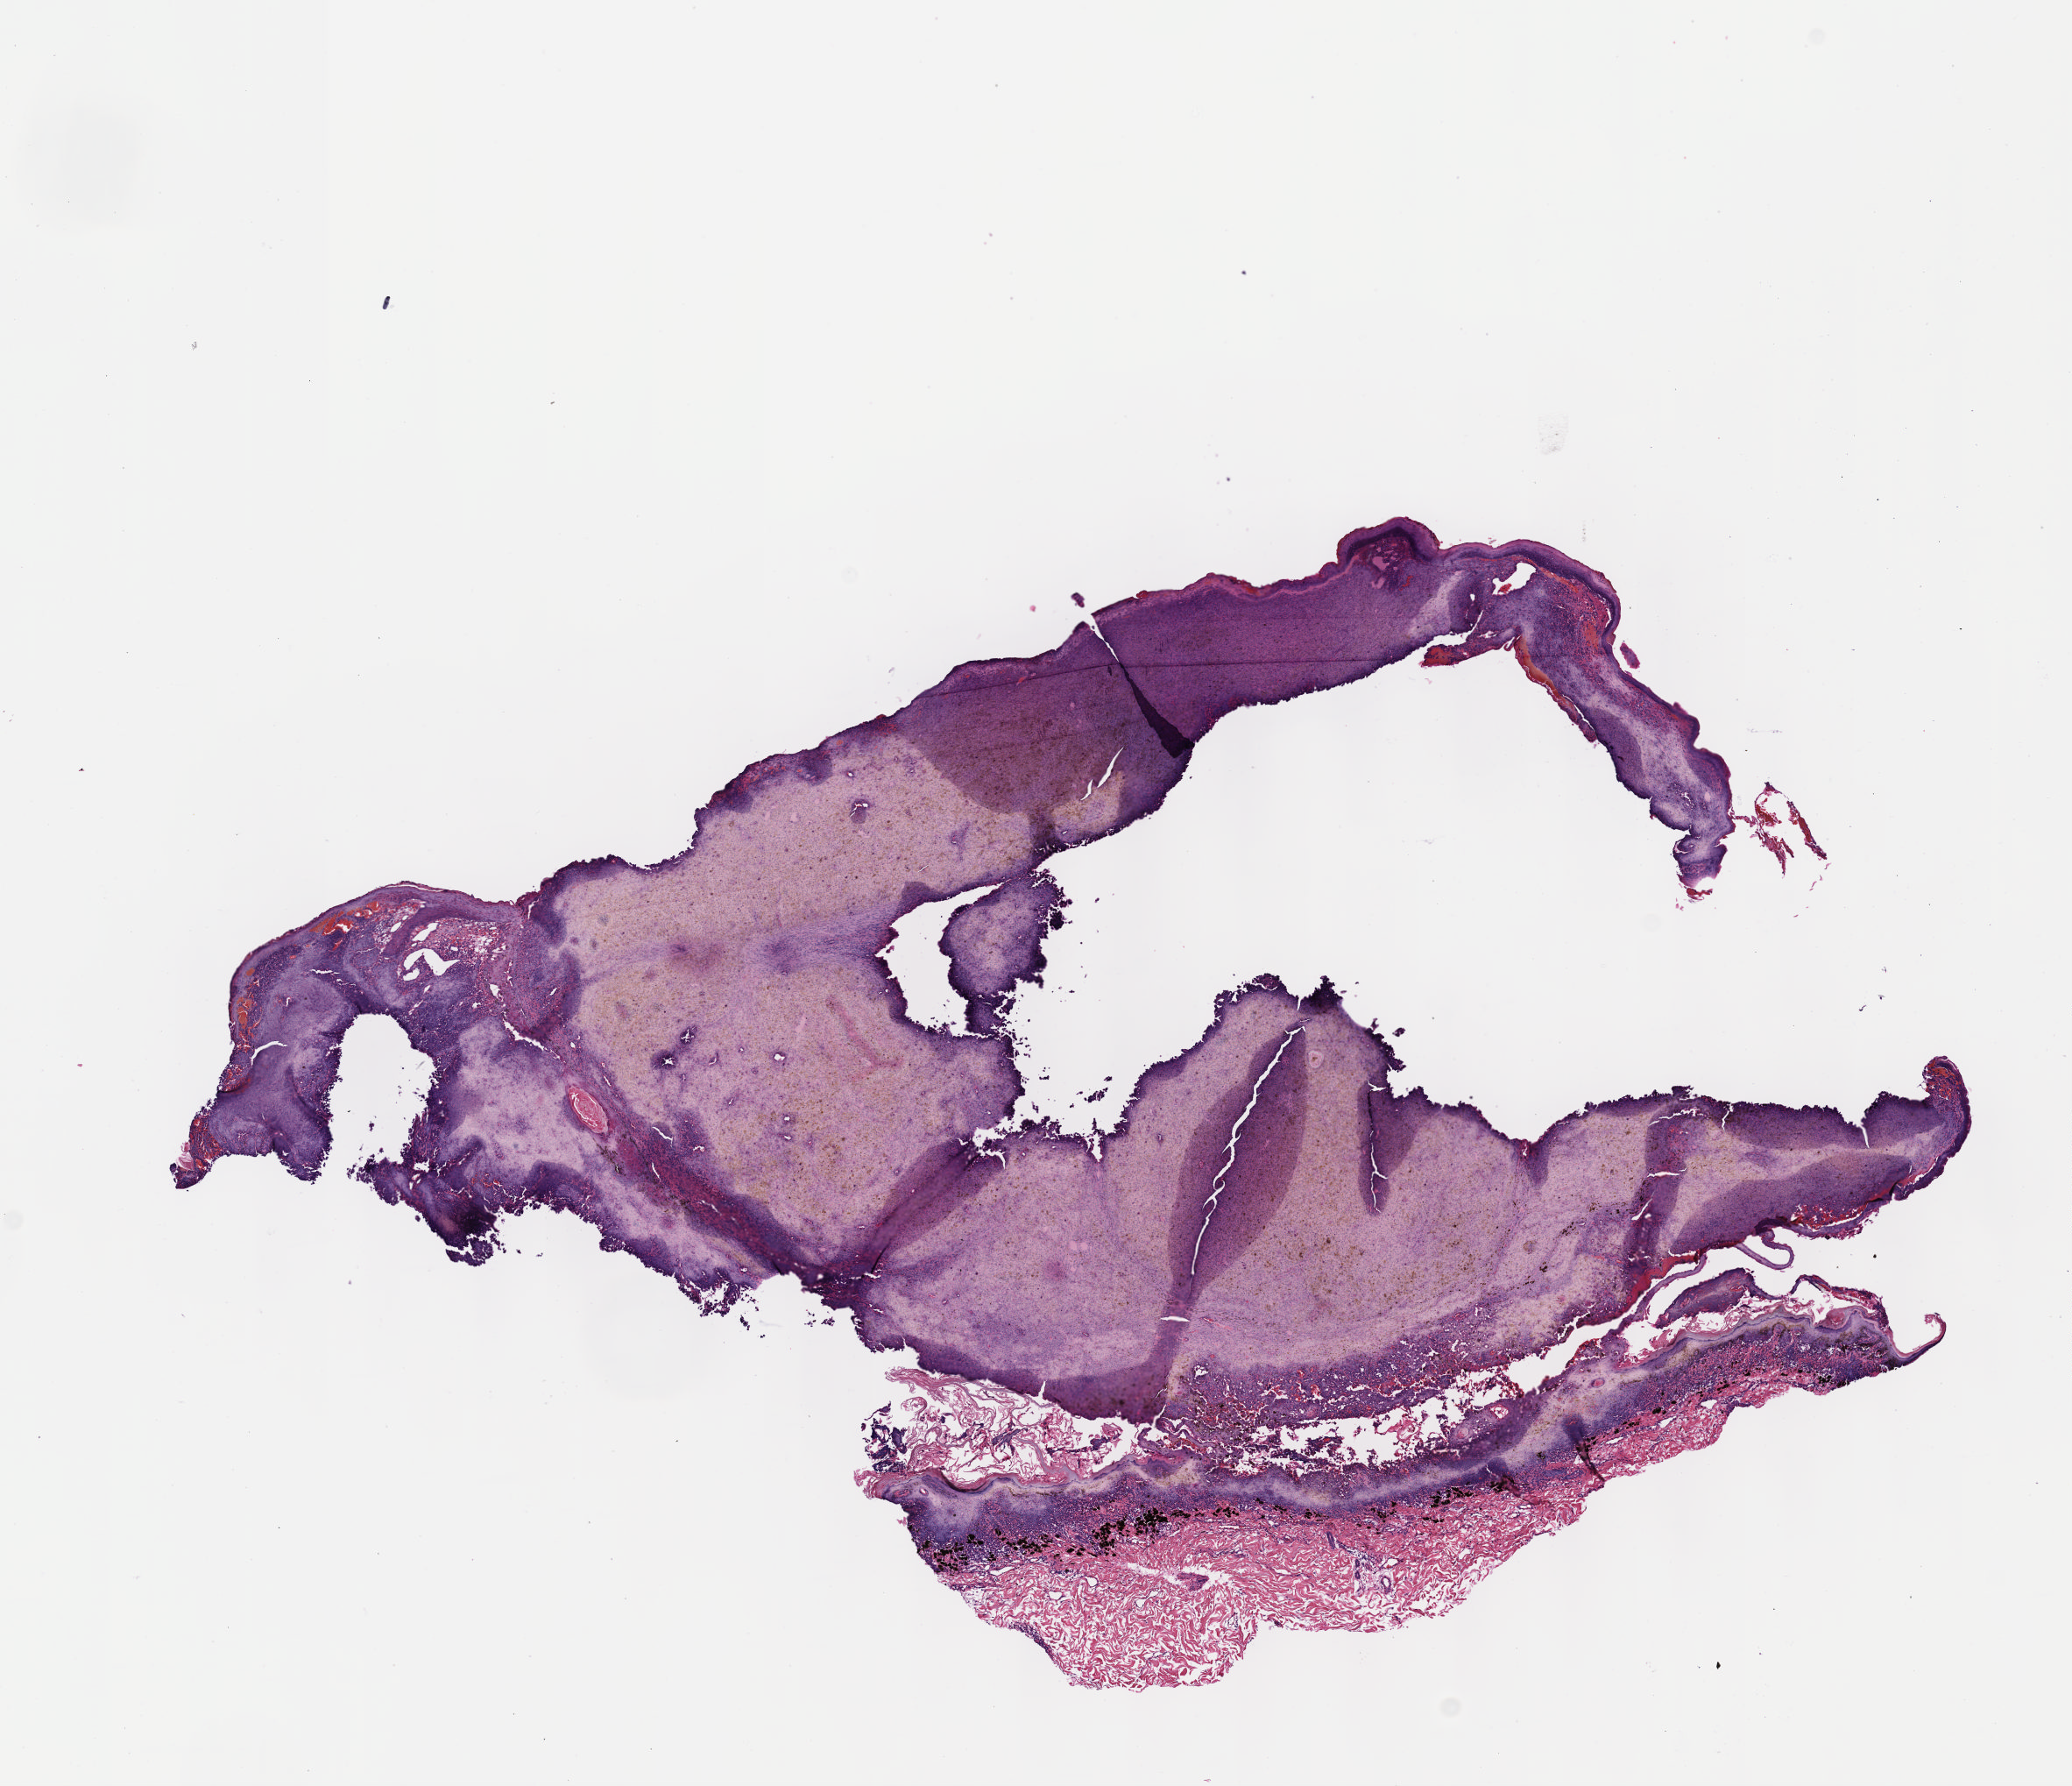
H&E-stained whole-slide image, shown as a low-resolution overview of the whole scanned area (about 9.6 x 8.2 mm, acquisition: 40x scan); formalin-fixed paraffin-embedded (FFPE) diagnostic section; skin, primary tumour sample. Female, age 74 years at initial diagnosis.
* AJCC pathologic stage: IIC
* TNM: T4b N0 M0
* histologic diagnosis: Malignant melanoma, NOS